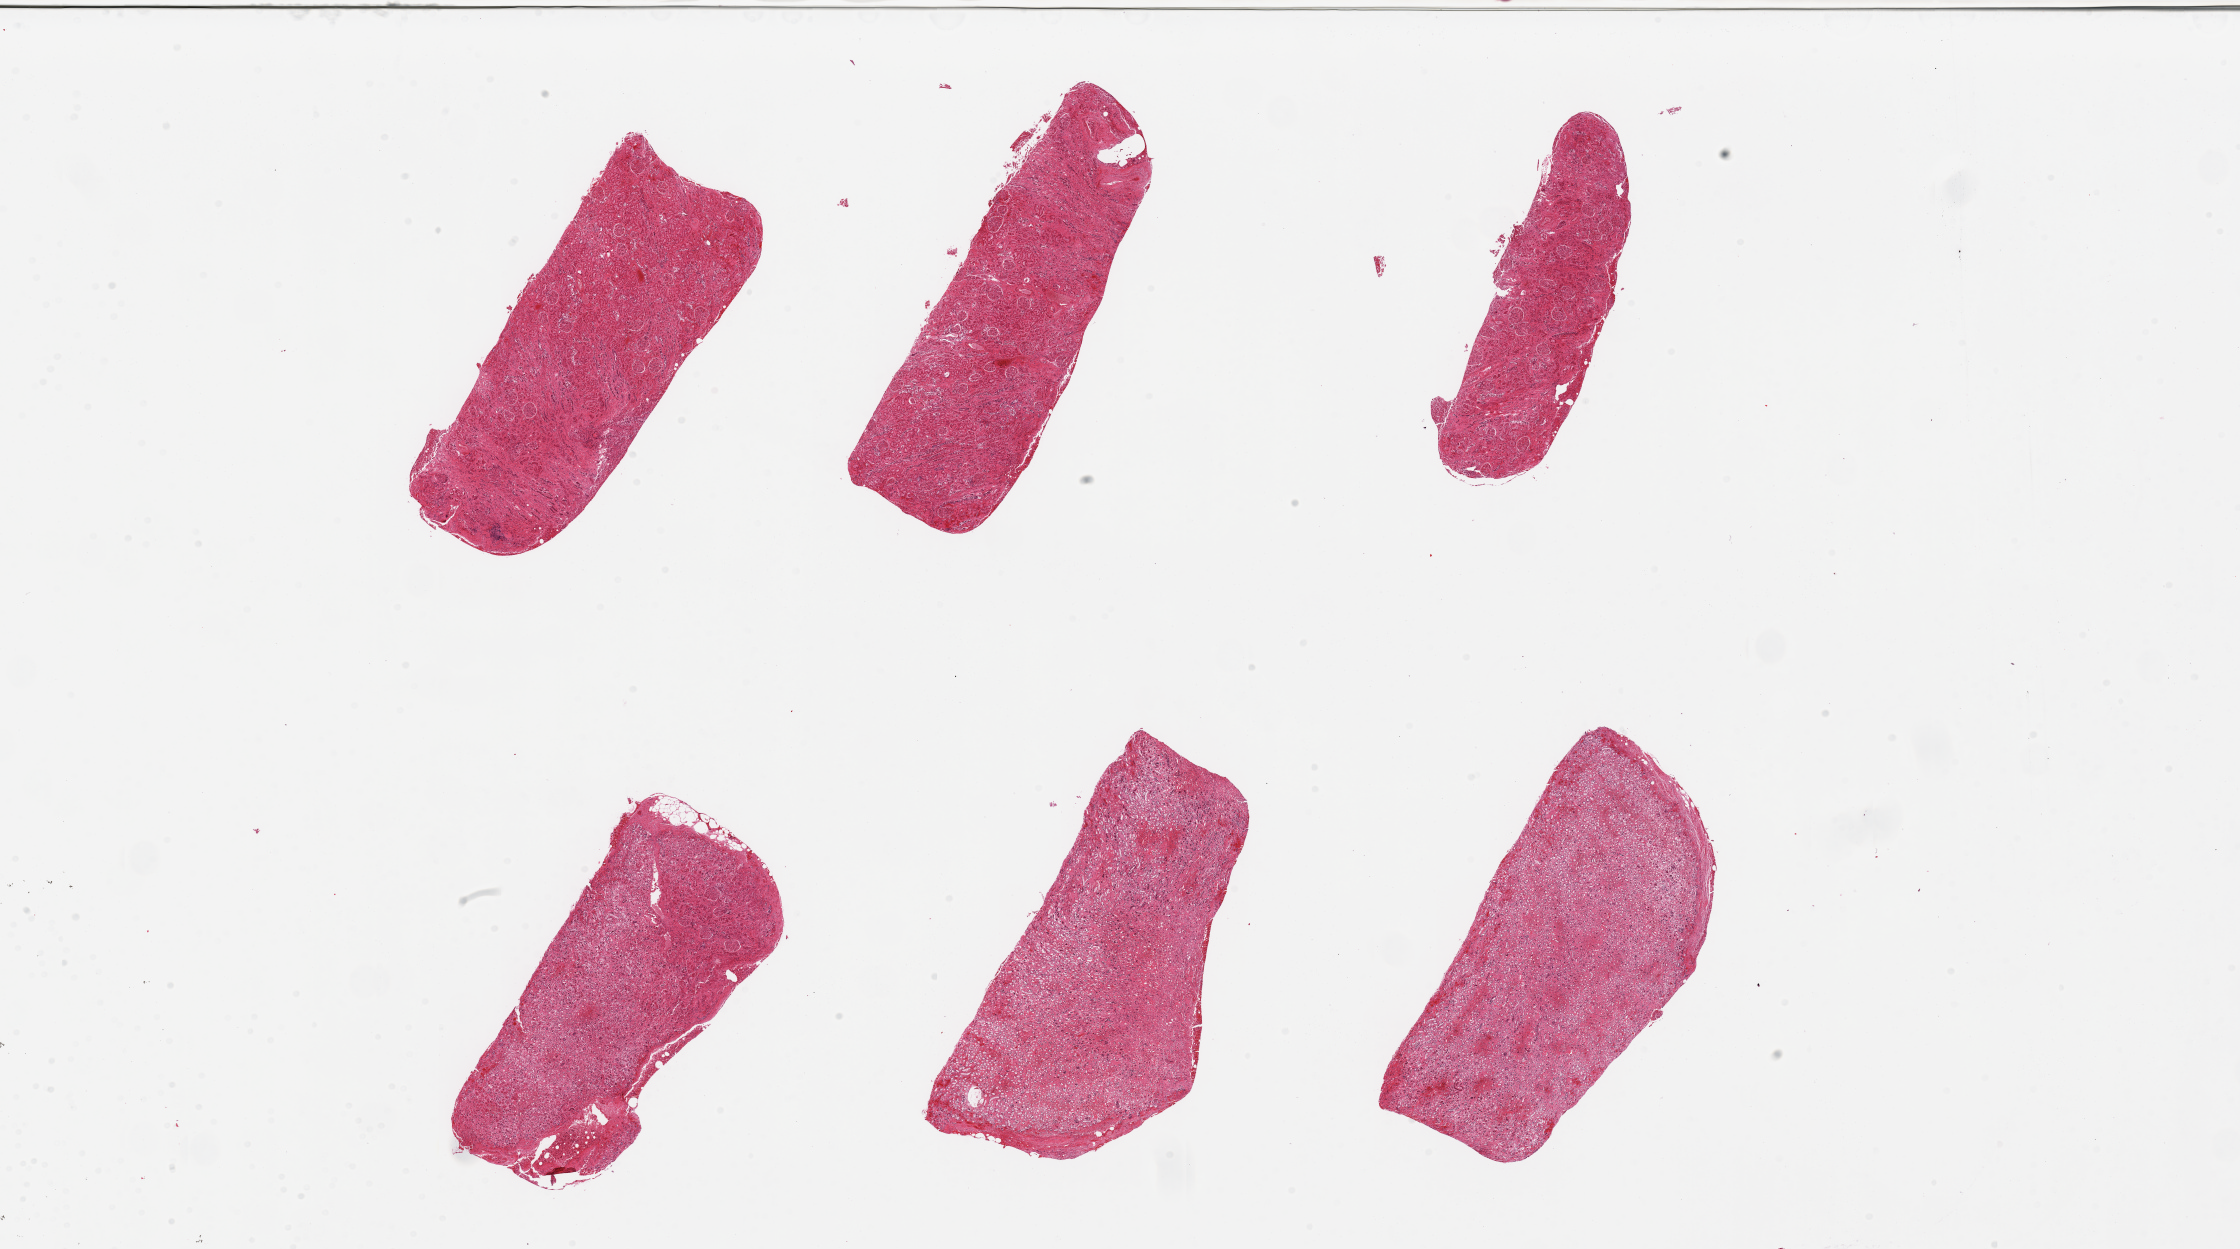
Whole-slide image, haematoxylin and eosin stain — low-resolution overview of the scanned area, about 35.4 x 19.8 mm, PAXgene-fixed paraffin-embedded (PFPE) section, section of renal cortex (target tissue), donor tissue sample. Donor sex: male.
Reviewer comment on this tissue sample: 6 pieces, renal cortex and medulla.